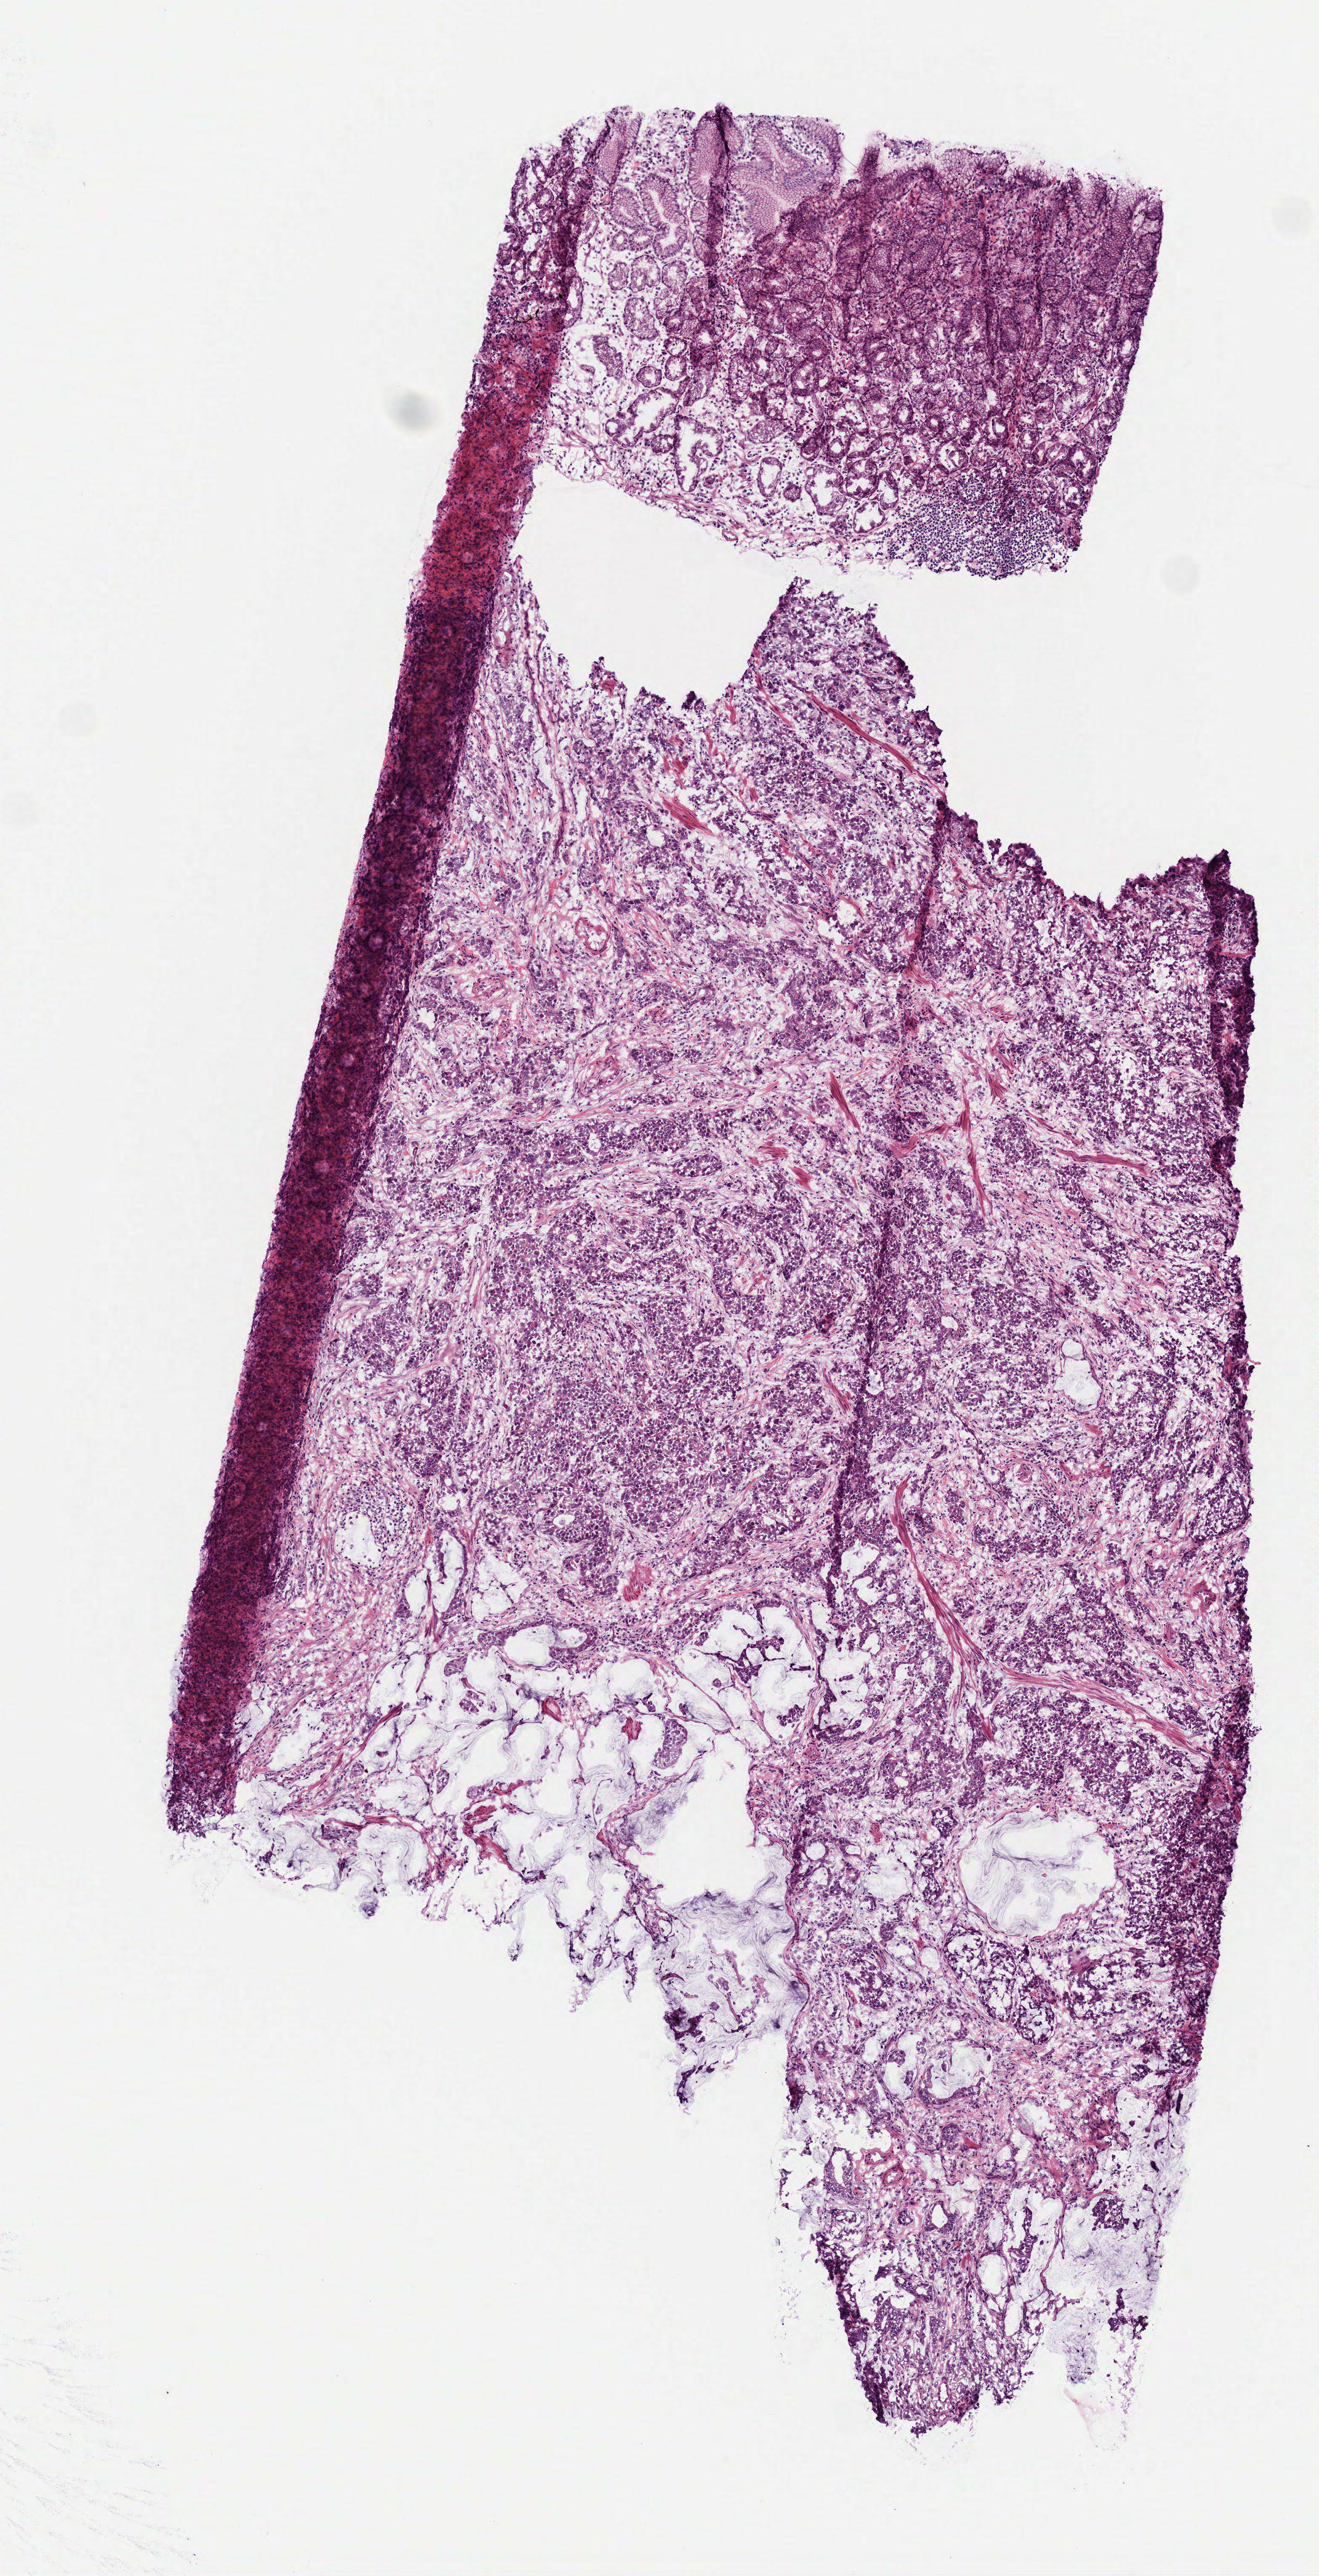
Hematoxylin and eosin (H&E) stained whole-slide image — shown as a low-resolution overview of the whole scanned area (about 3.1 x 6.1 mm, acquisition: 40x scan); frozen section from the top of the tissue portion; primary tumour sample from the stomach. Male patient. Histologic grade: G2 (moderately differentiated). Pathologist review of this section (percent, as recorded): tumour cells 87%, tumour nuclei 70%, normal cells 13%, stromal cells 0%, necrosis 0%. Infiltration values recorded for this section: lymphocyte infiltration 10%, monocyte infiltration 2%, neutrophil infiltration 5%.
Pathologic diagnosis: Mucinous adenocarcinoma (gastric antrum). Lymph nodes positive (case pathology): 2 of 8 examined. AJCC pathologic stage: II (6th edition).